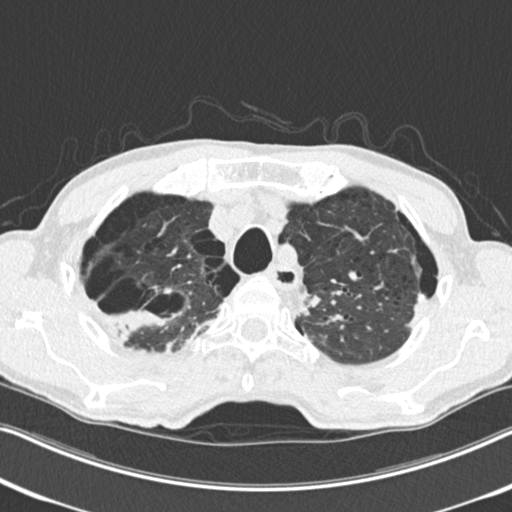
Low-dose screening chest CT, one axial slice; slice 205 of 251 in the series (ordered by position); 120 kVp; lung window (W 1500 / L -600 HU); 2 mm slice thickness; 512 × 512 image matrix.
Outlined on this slice (outlined manually by an expert reader):
- lesion 1 (tumor, upper lobe of right lung): bounding box <107,309,170,334> (left, top, right, bottom; pixels)